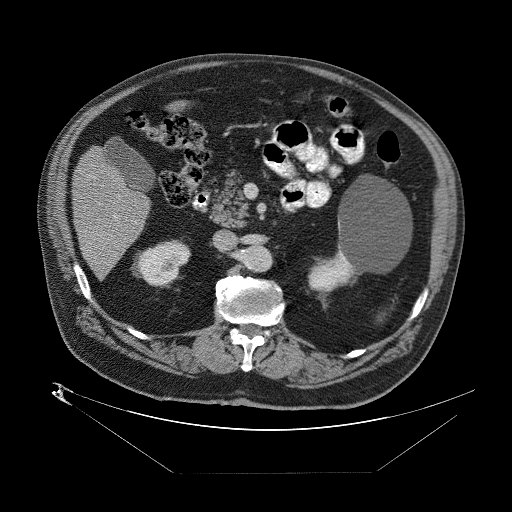
Contrast-enhanced abdominal CT (liver protocol), one axial slice. Slice 27 of 89 in the series (ordered by position). Reconstruction kernel STANDARD. One of 2 acquisitions stored at this slice position. Soft-tissue window (W 400 / L 40 HU). 512 × 512 image matrix, field of view 480 × 480 mm. Case-level facts recorded for this patient, not image findings: diagnosis: hepatocellular carcinoma (patient treated with transarterial chemoembolisation; whether this scan precedes or follows treatment is not stated here); TNM stage (as recorded): Stage-II; Child-Pugh class: B; tumour nodularity: multinodular; tumour size: 4 cm.
Structures marked on this image (semi-automatically segmented with operator editing):
- abdominal aorta: box from (x=246, y=248) to (x=269, y=272) px
- liver parenchyma outside the tumour (the mass and vessels are separate outlines, so this box may not span the whole liver): (x=70, y=142)–(x=150, y=278)
- liver vessels: (x=84, y=211)–(x=118, y=255)